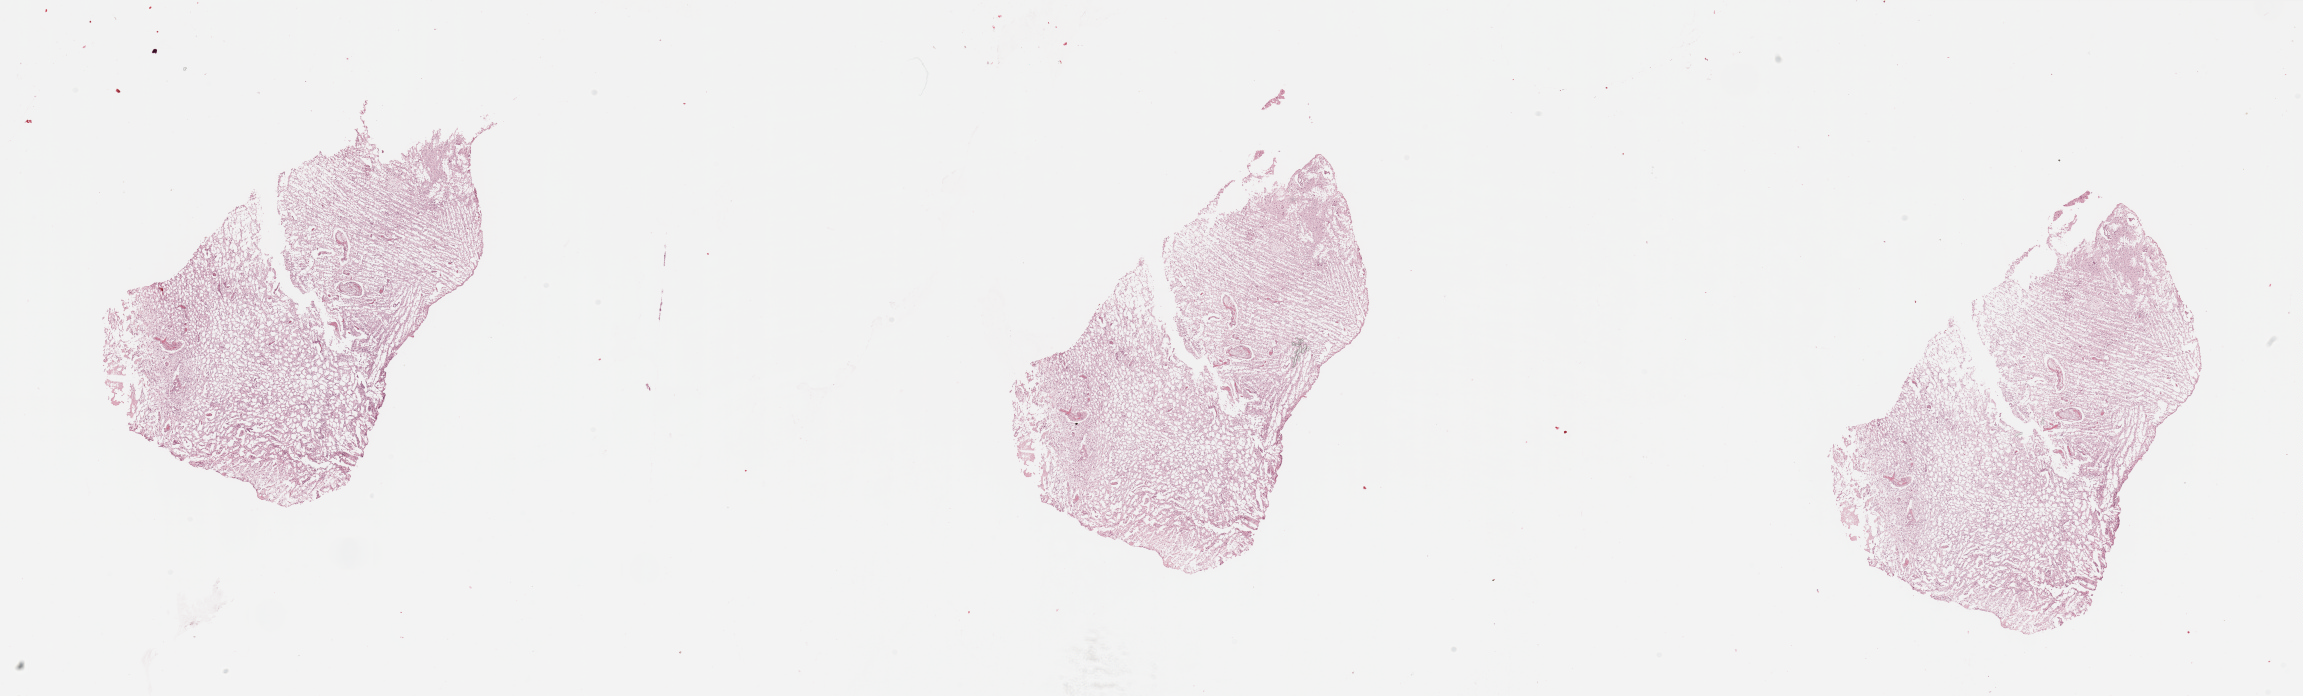
Digitized H&E-stained tissue section (whole slide), a low-resolution overview of the entire scanned area, about 36.4 x 11.0 mm (from a 20x scan); tumour tissue sample, sampled site: brain. 58-year-old male patient. Pathologist review of this section (percent, as recorded): tumour nuclei 80%, necrosis 5%.
Primary tumour site (as recorded): temporal lobe. Diagnosis: Glioblastoma.